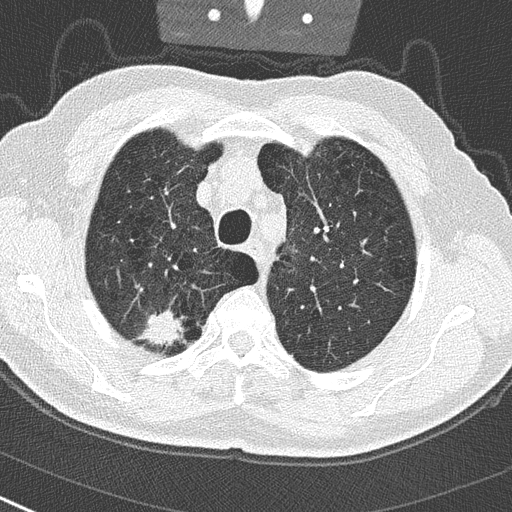
Low-dose screening chest CT, one axial slice; position 234 of 290 along the scan axis; reconstruction kernel B50f; 120 kVp; lung window (W 1500 / L -600 HU); 2 mm slice thickness; 512 × 512 image matrix.
Structures marked on this image (expert manual segmentation):
- lesion 1 (tumor, upper lobe of right lung): bounding box <140,311,185,349> (left, top, right, bottom; pixels)